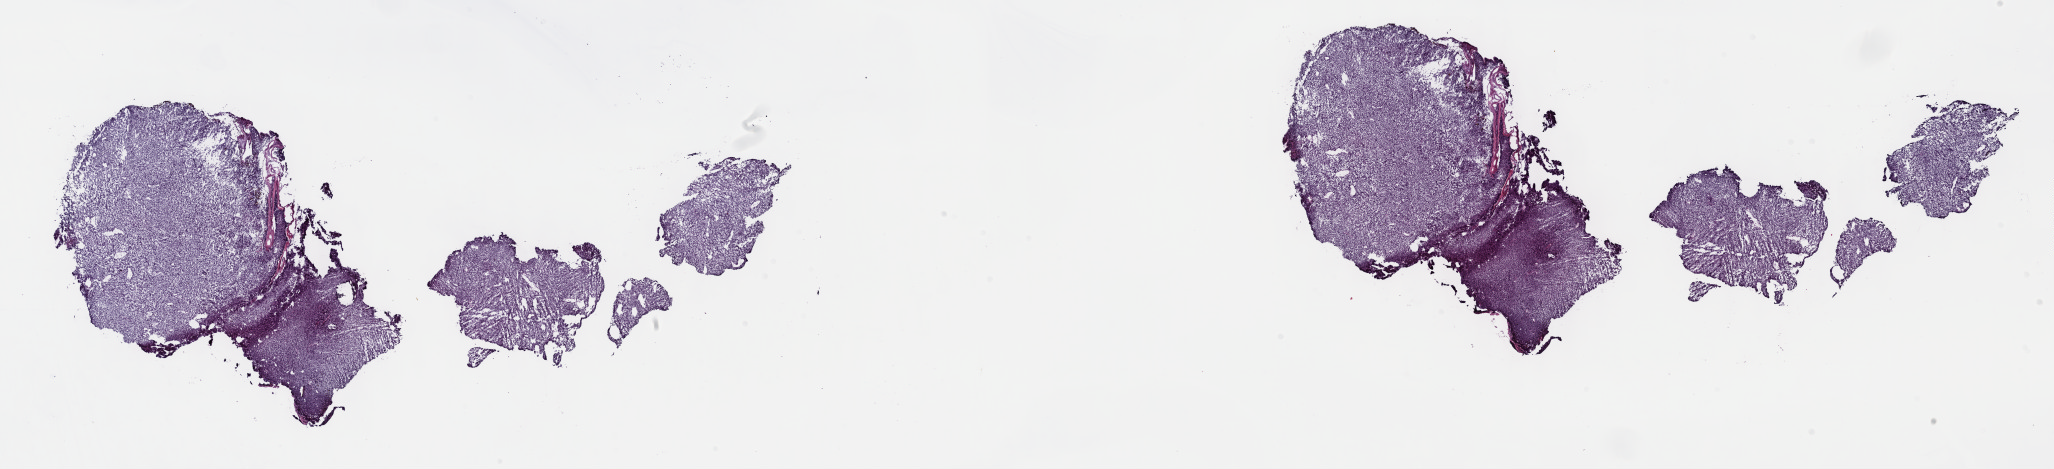
Digitized H&E tissue section (whole slide), a low-resolution overview of the entire scanned area, about 33.2 x 7.6 mm (slide scanned at 40x). Frozen section from the top of the tissue portion. Primary tumour sample from the uvea. Patient: female, age at initial diagnosis 78 years.
Pathologic diagnosis: Mixed epithelioid and spindle cell melanoma.